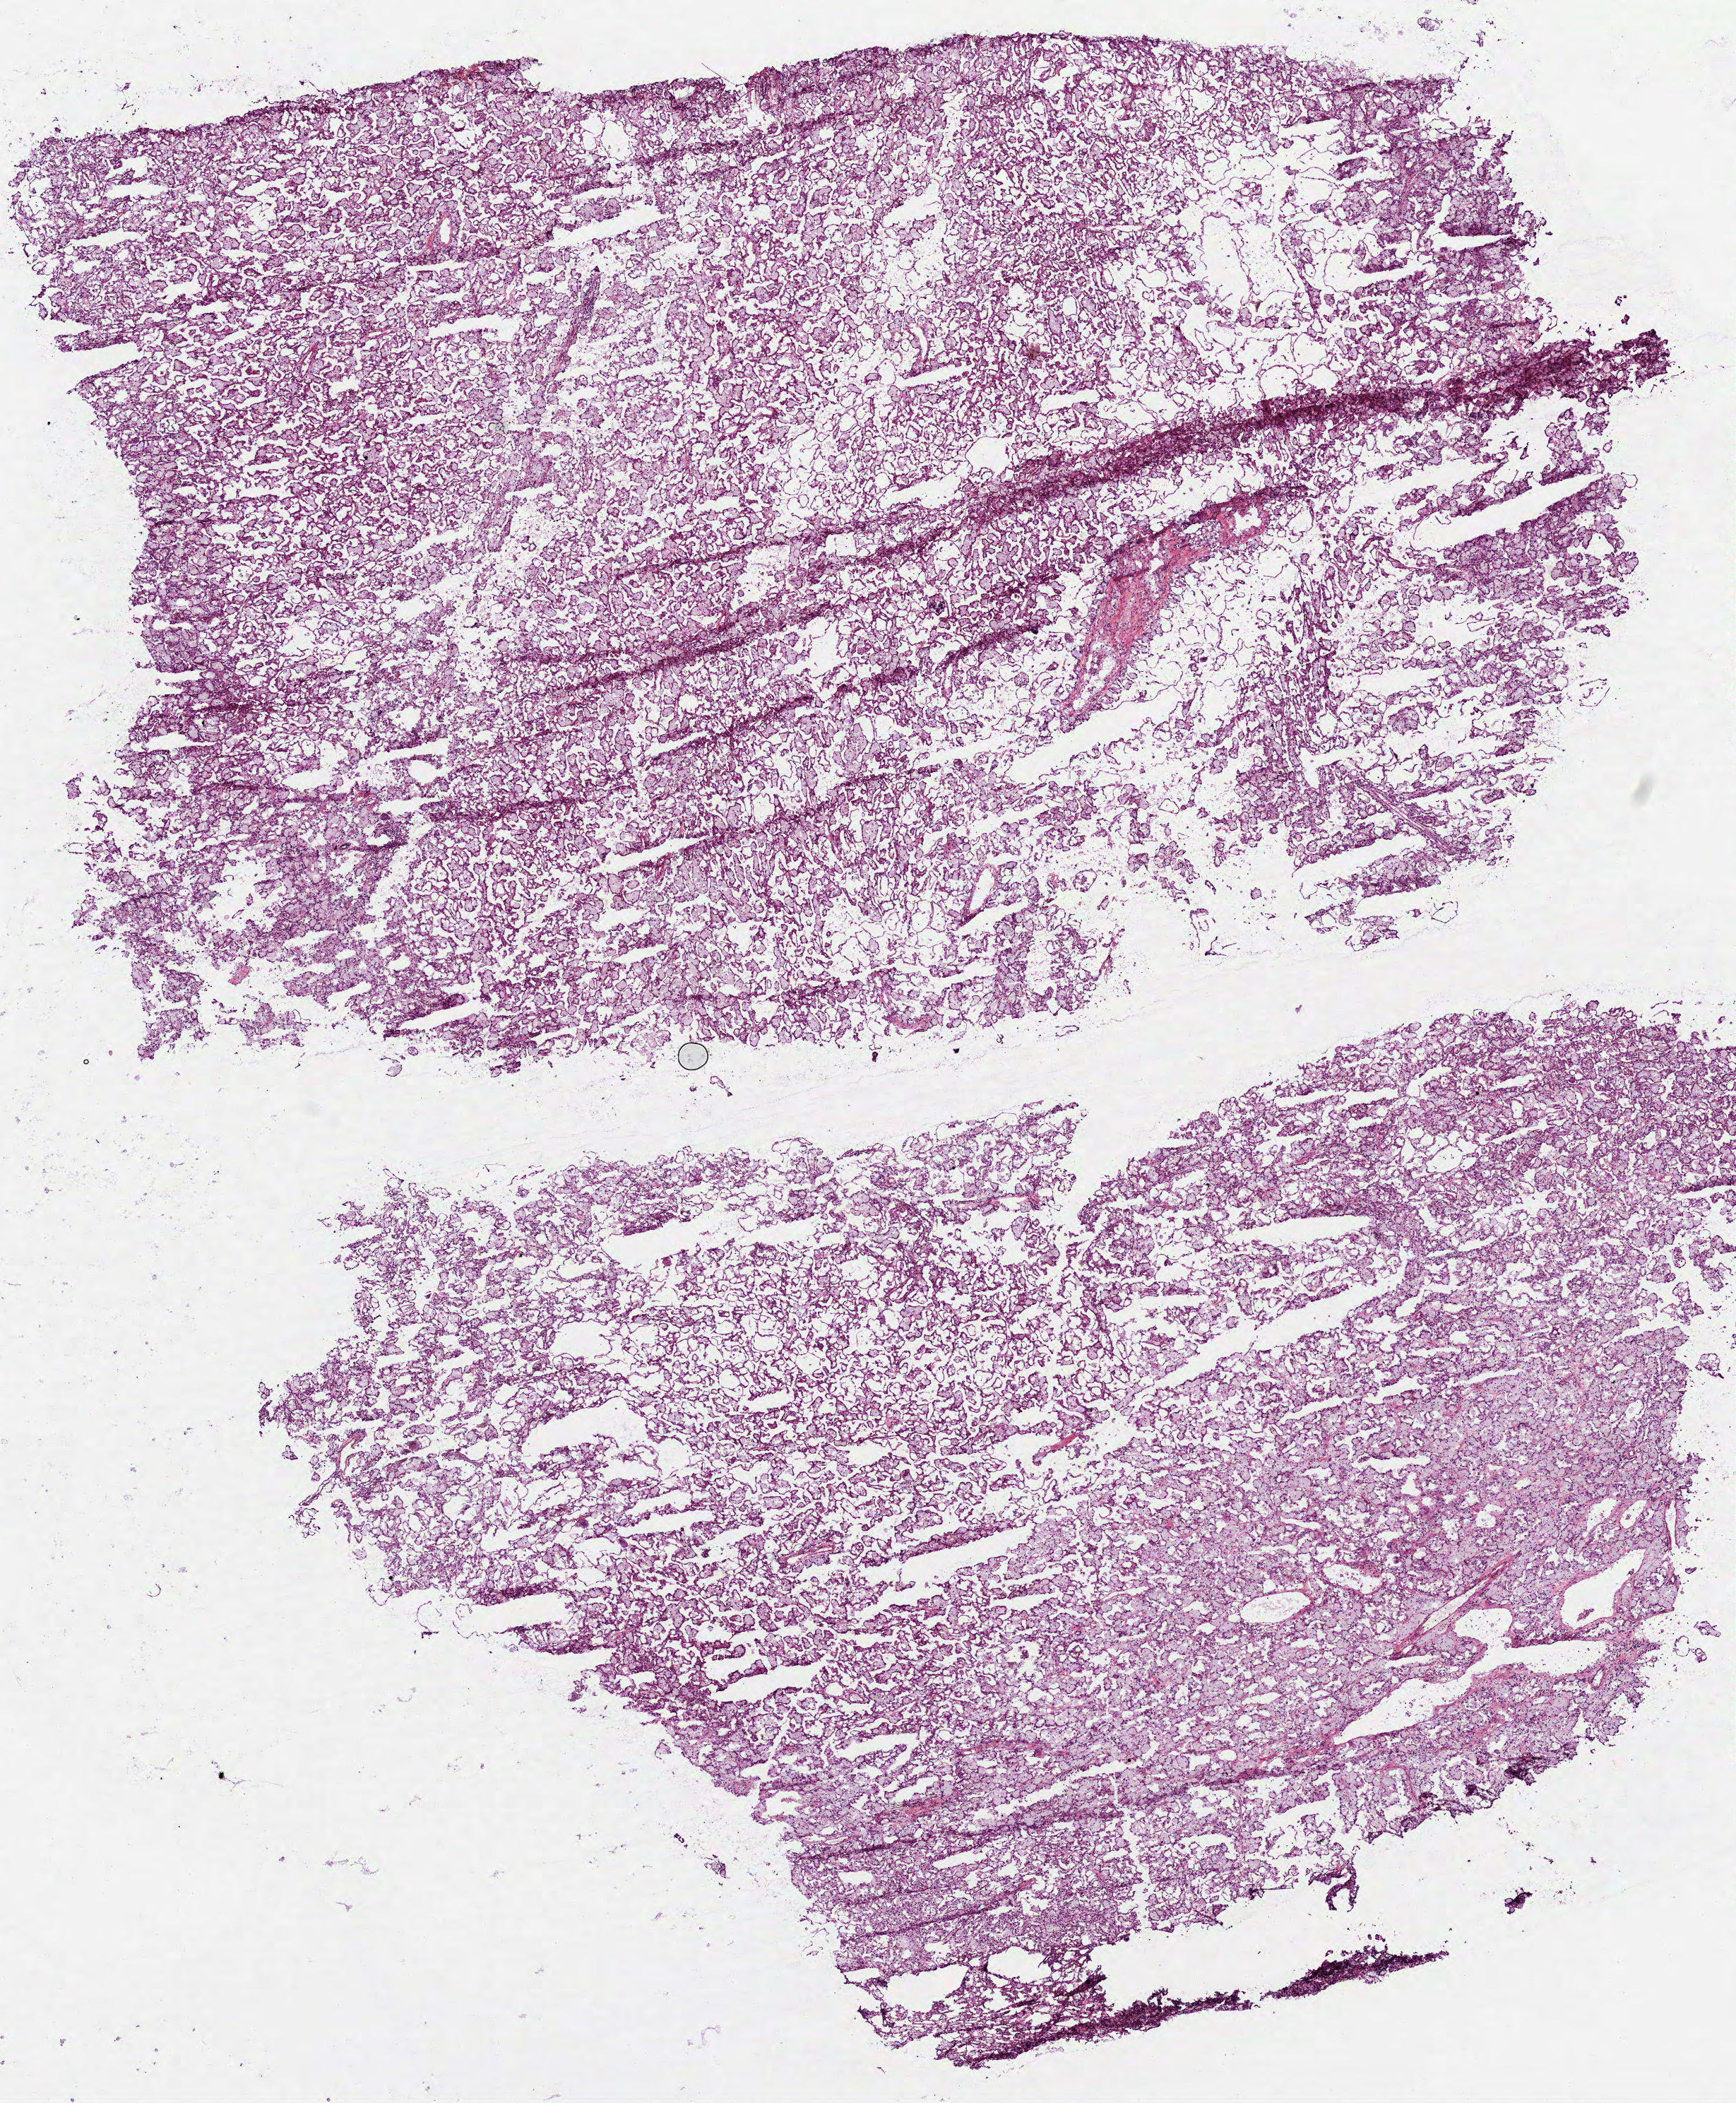
Digitized Hematoxylin and eosin (H&E) stained tissue section (whole slide), whole scanned area (about 9.9 x 12.0 mm, from a 40x scan) shown as a low-resolution overview, frozen section from the top of the tissue portion, sample: primary tumour, kidney. Patient: female, age at initial diagnosis 60 years. Slide review estimates, as recorded: tumour cells 98%, tumour nuclei 85%.
Pathologic diagnosis: Papillary adenocarcinoma, NOS.